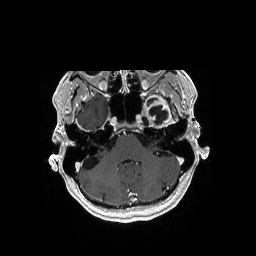
Brain MRI from a brain-tumour surgery series, one axial slice. Slice 135 of 176 in the series (ordered by position). T1-weighted post-contrast. 1 mm slice thickness. 256 × 256 image matrix, field of view 256 × 256 mm. Case-level facts recorded for this patient, not image findings: histopathology: Glioblastoma; WHO grade: 4; IDH mutation: no; tumour location: Left Medial Temporal.
Annotated regions visible in this slice (outlined manually by an expert reader):
- previous resection cavity: bounding box [x1, y1, x2, y2] px = [148, 106, 167, 122]